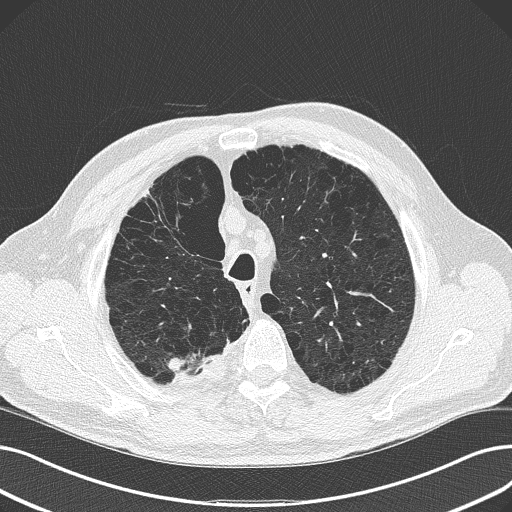
Low-dose screening chest CT, axial slice. Second annual screen. Lung window (W 1500 / L -600 HU). Slice 42 of 165 in the series. Male, age 68 years at enrolment.
Expert reader's lesion annotation, box from (x=143, y=332) to (x=229, y=395) px. The screening reader recorded 4 non-calcified nodules or masses ≥4 mm on this exam; which of them this box marks is not recorded.